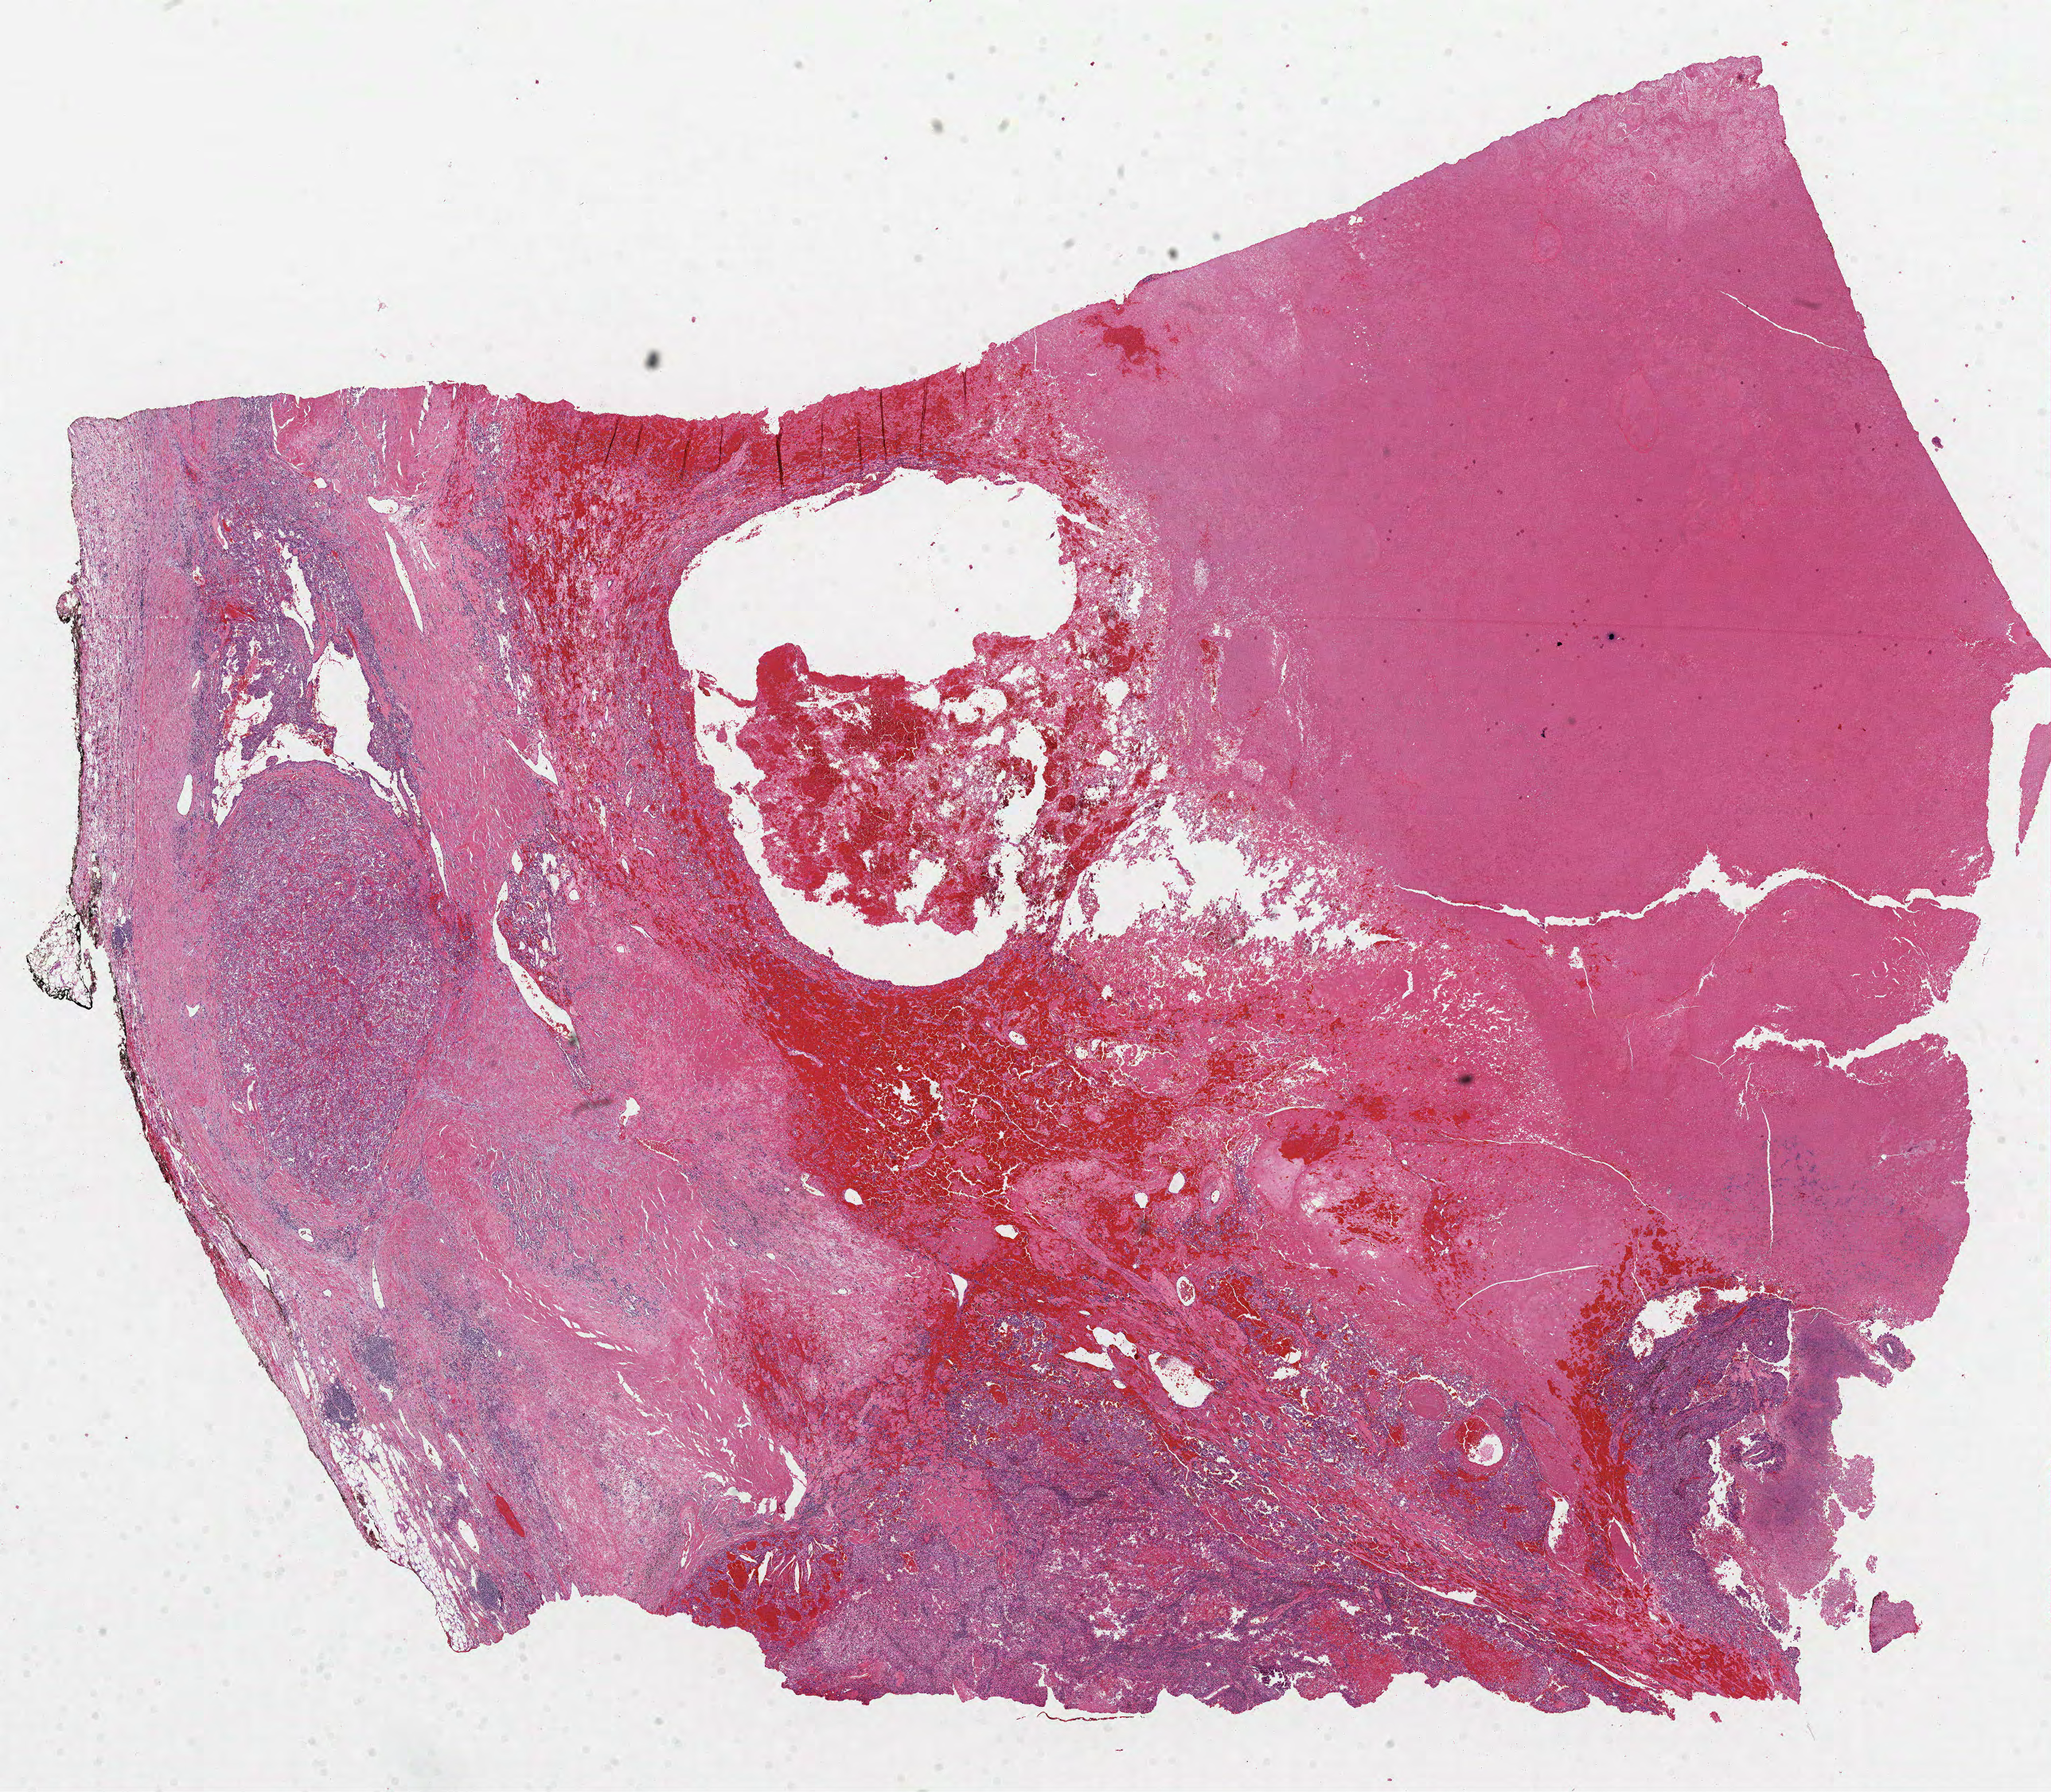
Whole-slide histology image, H&E — a low-resolution overview of the entire scanned area, about 20.8 x 18.2 mm (acquisition: 40x scan). FFPE section. Primary tumour sample from the kidney. Female patient; age at initial diagnosis 60 years. Histologic grade: G4 (undifferentiated).
* histologic diagnosis: Clear cell adenocarcinoma, NOS
* AJCC pathologic stage: IV